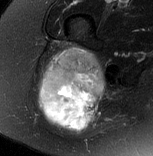
MRI of an extremity soft-tissue mass, one axial slice; position 48 of 77 along the scan axis; T2-weighted fat-saturated; MR volume resampled by the dataset authors to the PET/CT grid (not the native acquisition matrix); 153 × 156 image matrix, field of view 149 × 152 mm. Female patient. Case-level facts recorded for this patient, not image findings: histological type: synovial sarcoma; grade: intermediate; site of the primary tumour: right buttock.
Outlined on this slice (expert contour drawn on MRI and transferred to this co-registered scan by the dataset authors):
- gross tumour volume including surrounding oedema: bounding box (x1, y1, x2, y2) in pixels: (39, 47, 106, 133)
- gross tumour volume (mass): (39, 47, 106, 123)